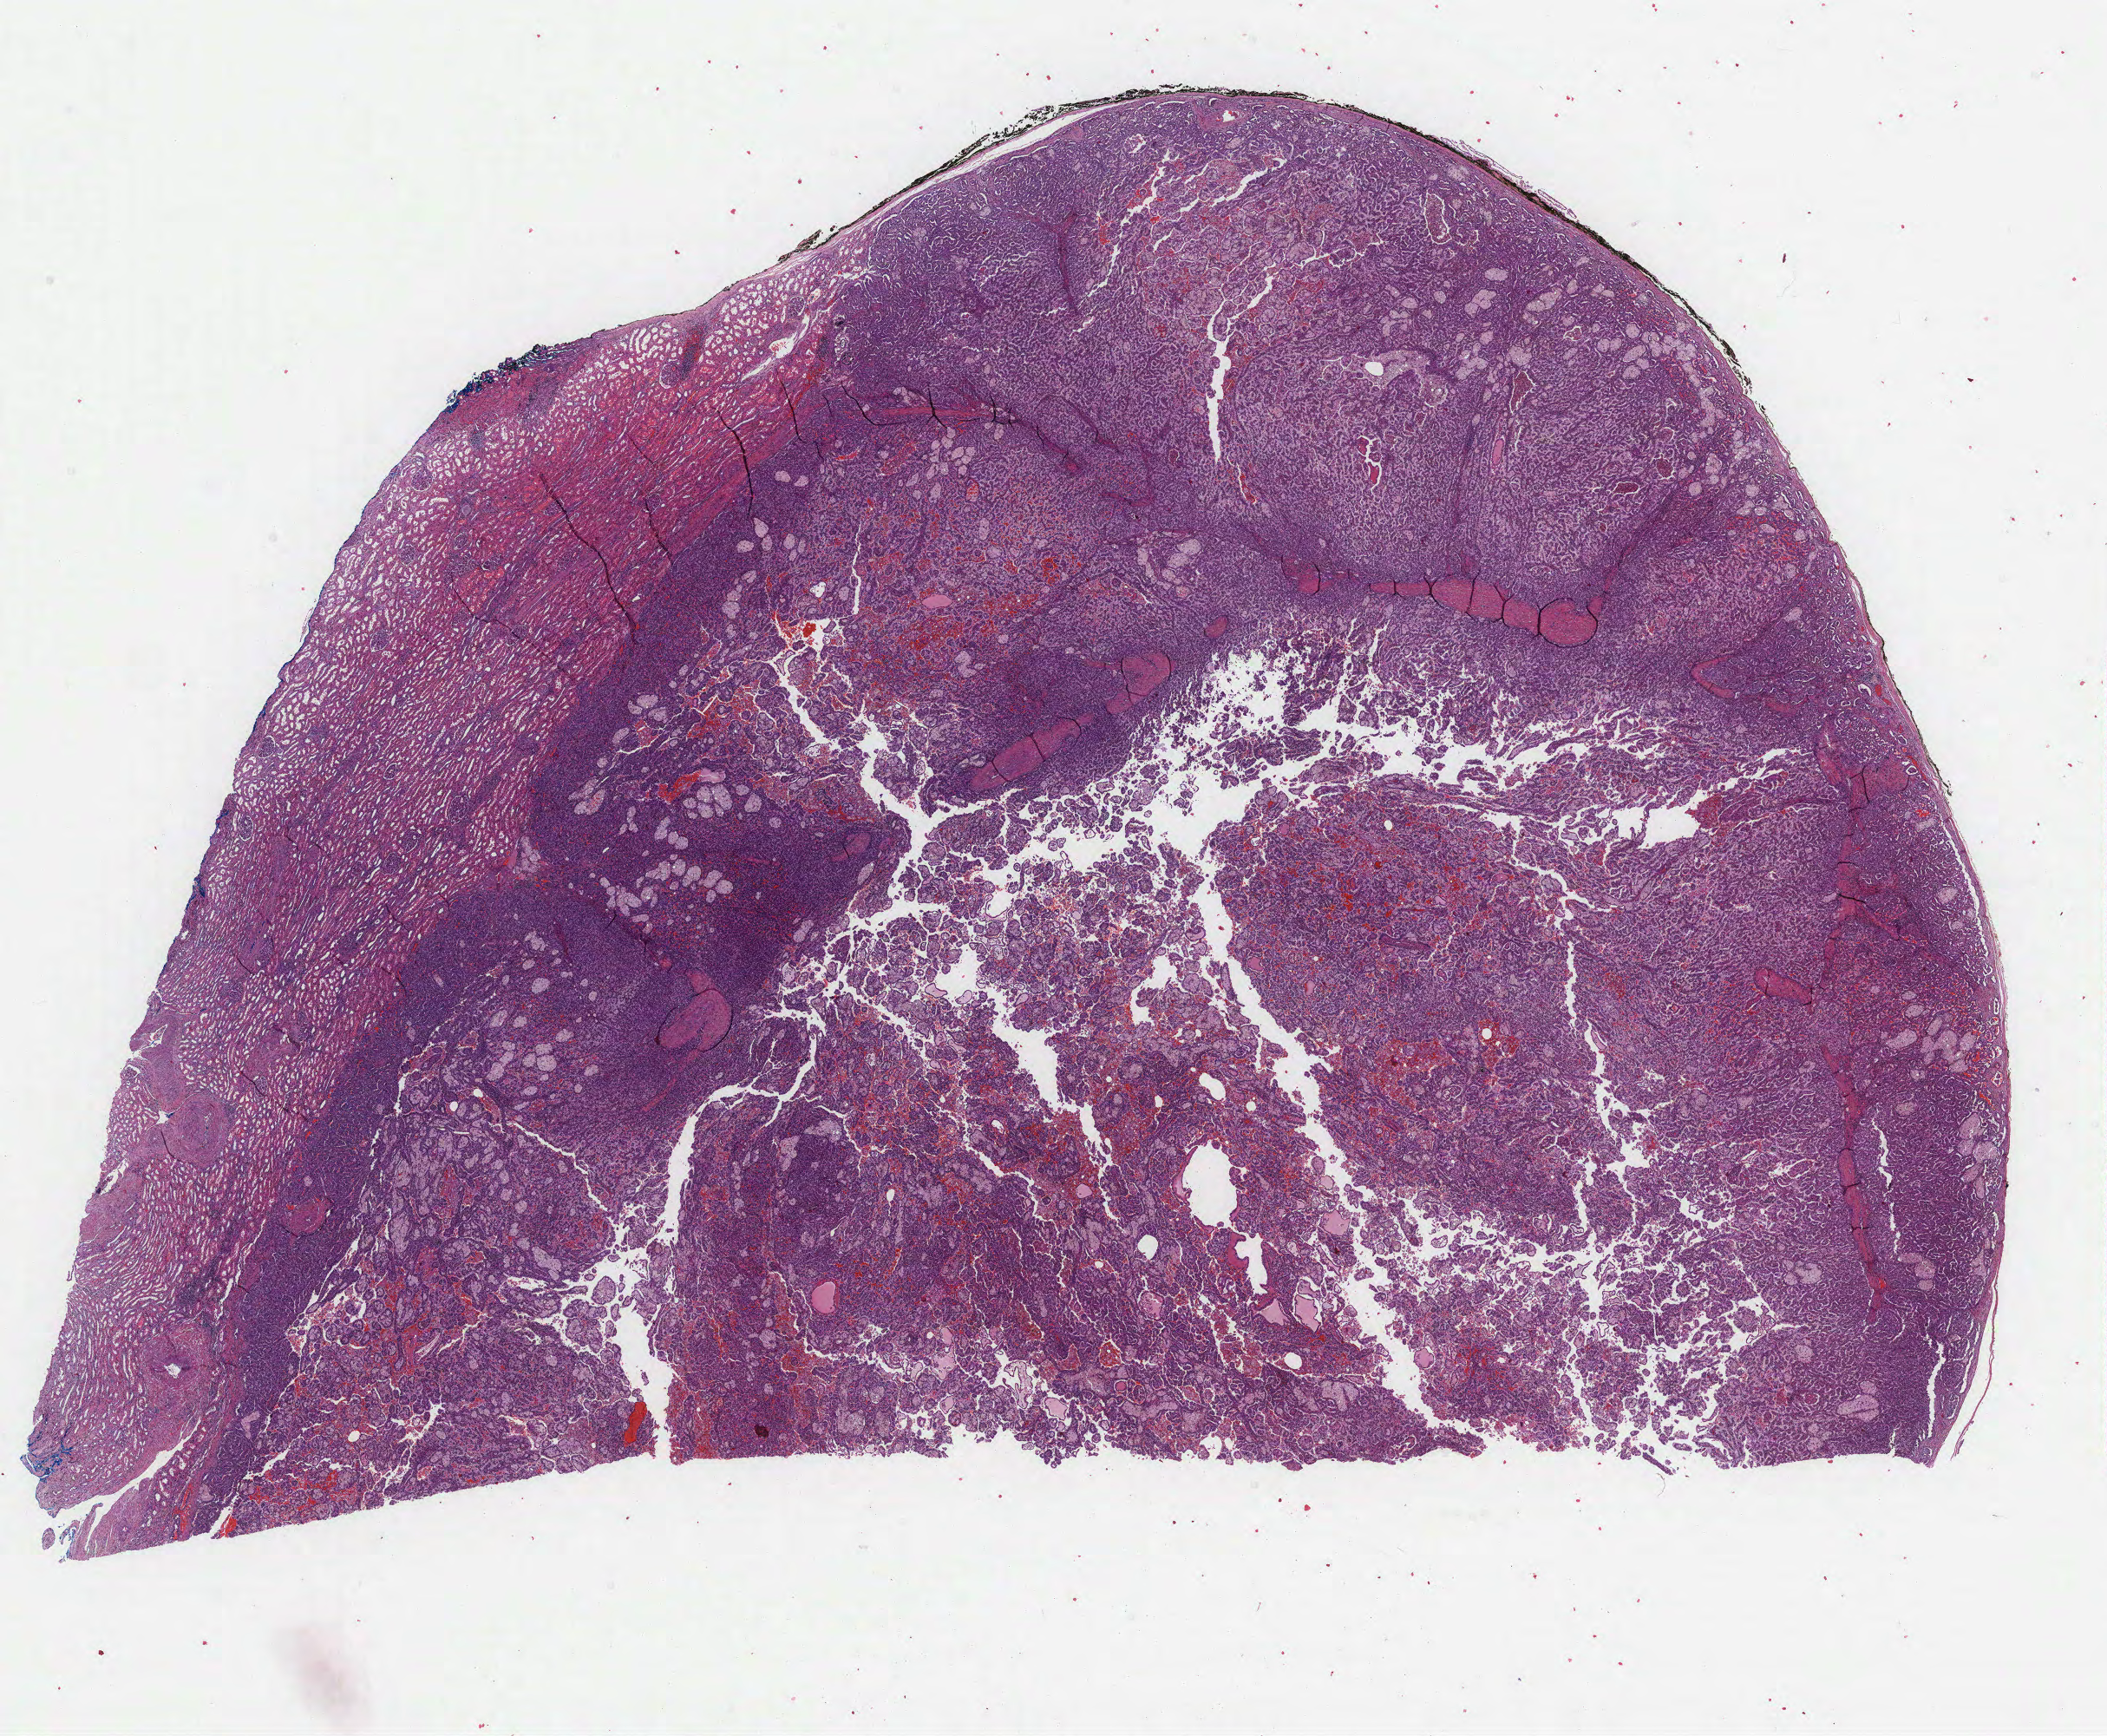
Digitized H&E-stained tissue section (whole slide), low-resolution overview of the scanned area, about 19.6 x 16.2 mm (slide scanned at 40x); formalin-fixed paraffin-embedded (FFPE) diagnostic section; kidney, primary tumour sample. Male, age 57 years at initial diagnosis.
AJCC pathologic stage: I (7th edition). Pathologic diagnosis: Papillary adenocarcinoma, NOS.